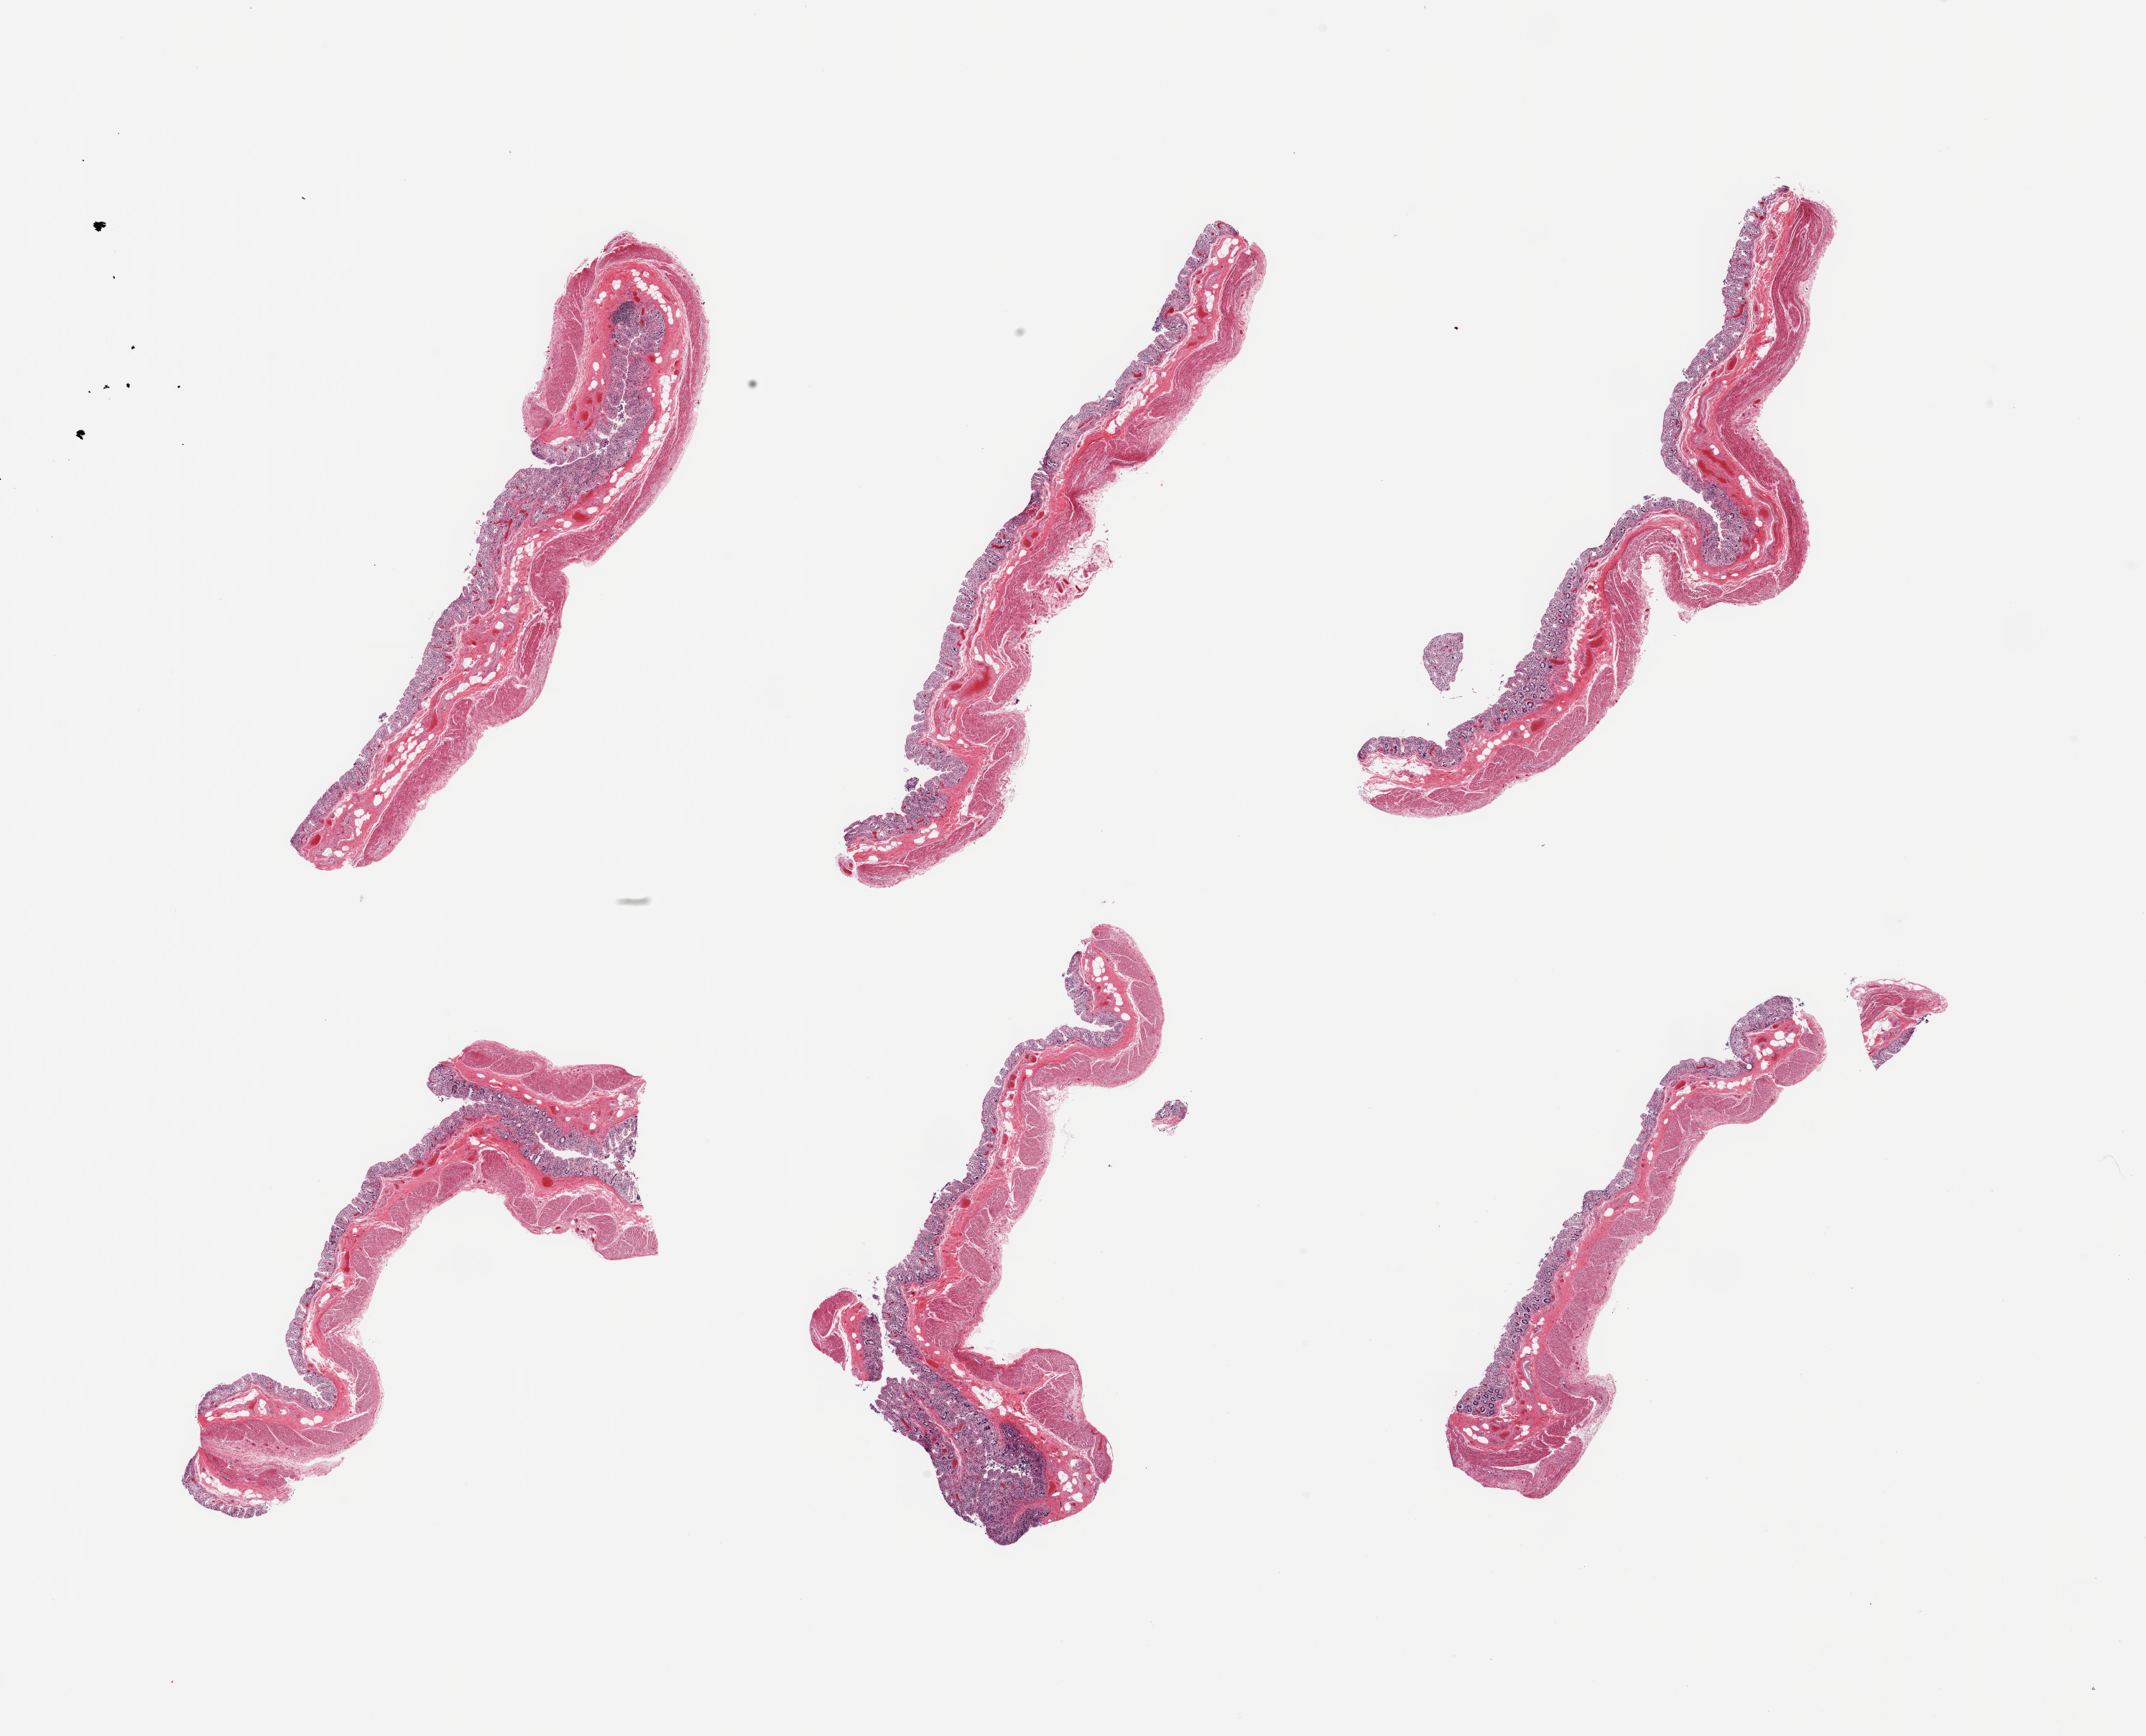
Whole-slide image, haematoxylin and eosin stain, brightfield, a low-resolution overview of the entire scanned area, about 23.6 x 19.1 mm. PAXgene-fixed paraffin-embedded (PFPE) section. Section of transverse colon (target tissue). Tissue donor sample. Donor sex: male.
Reviewer comment on this tissue sample: 6 pieces; autolyzed mucosa, muscularis is better preserved.